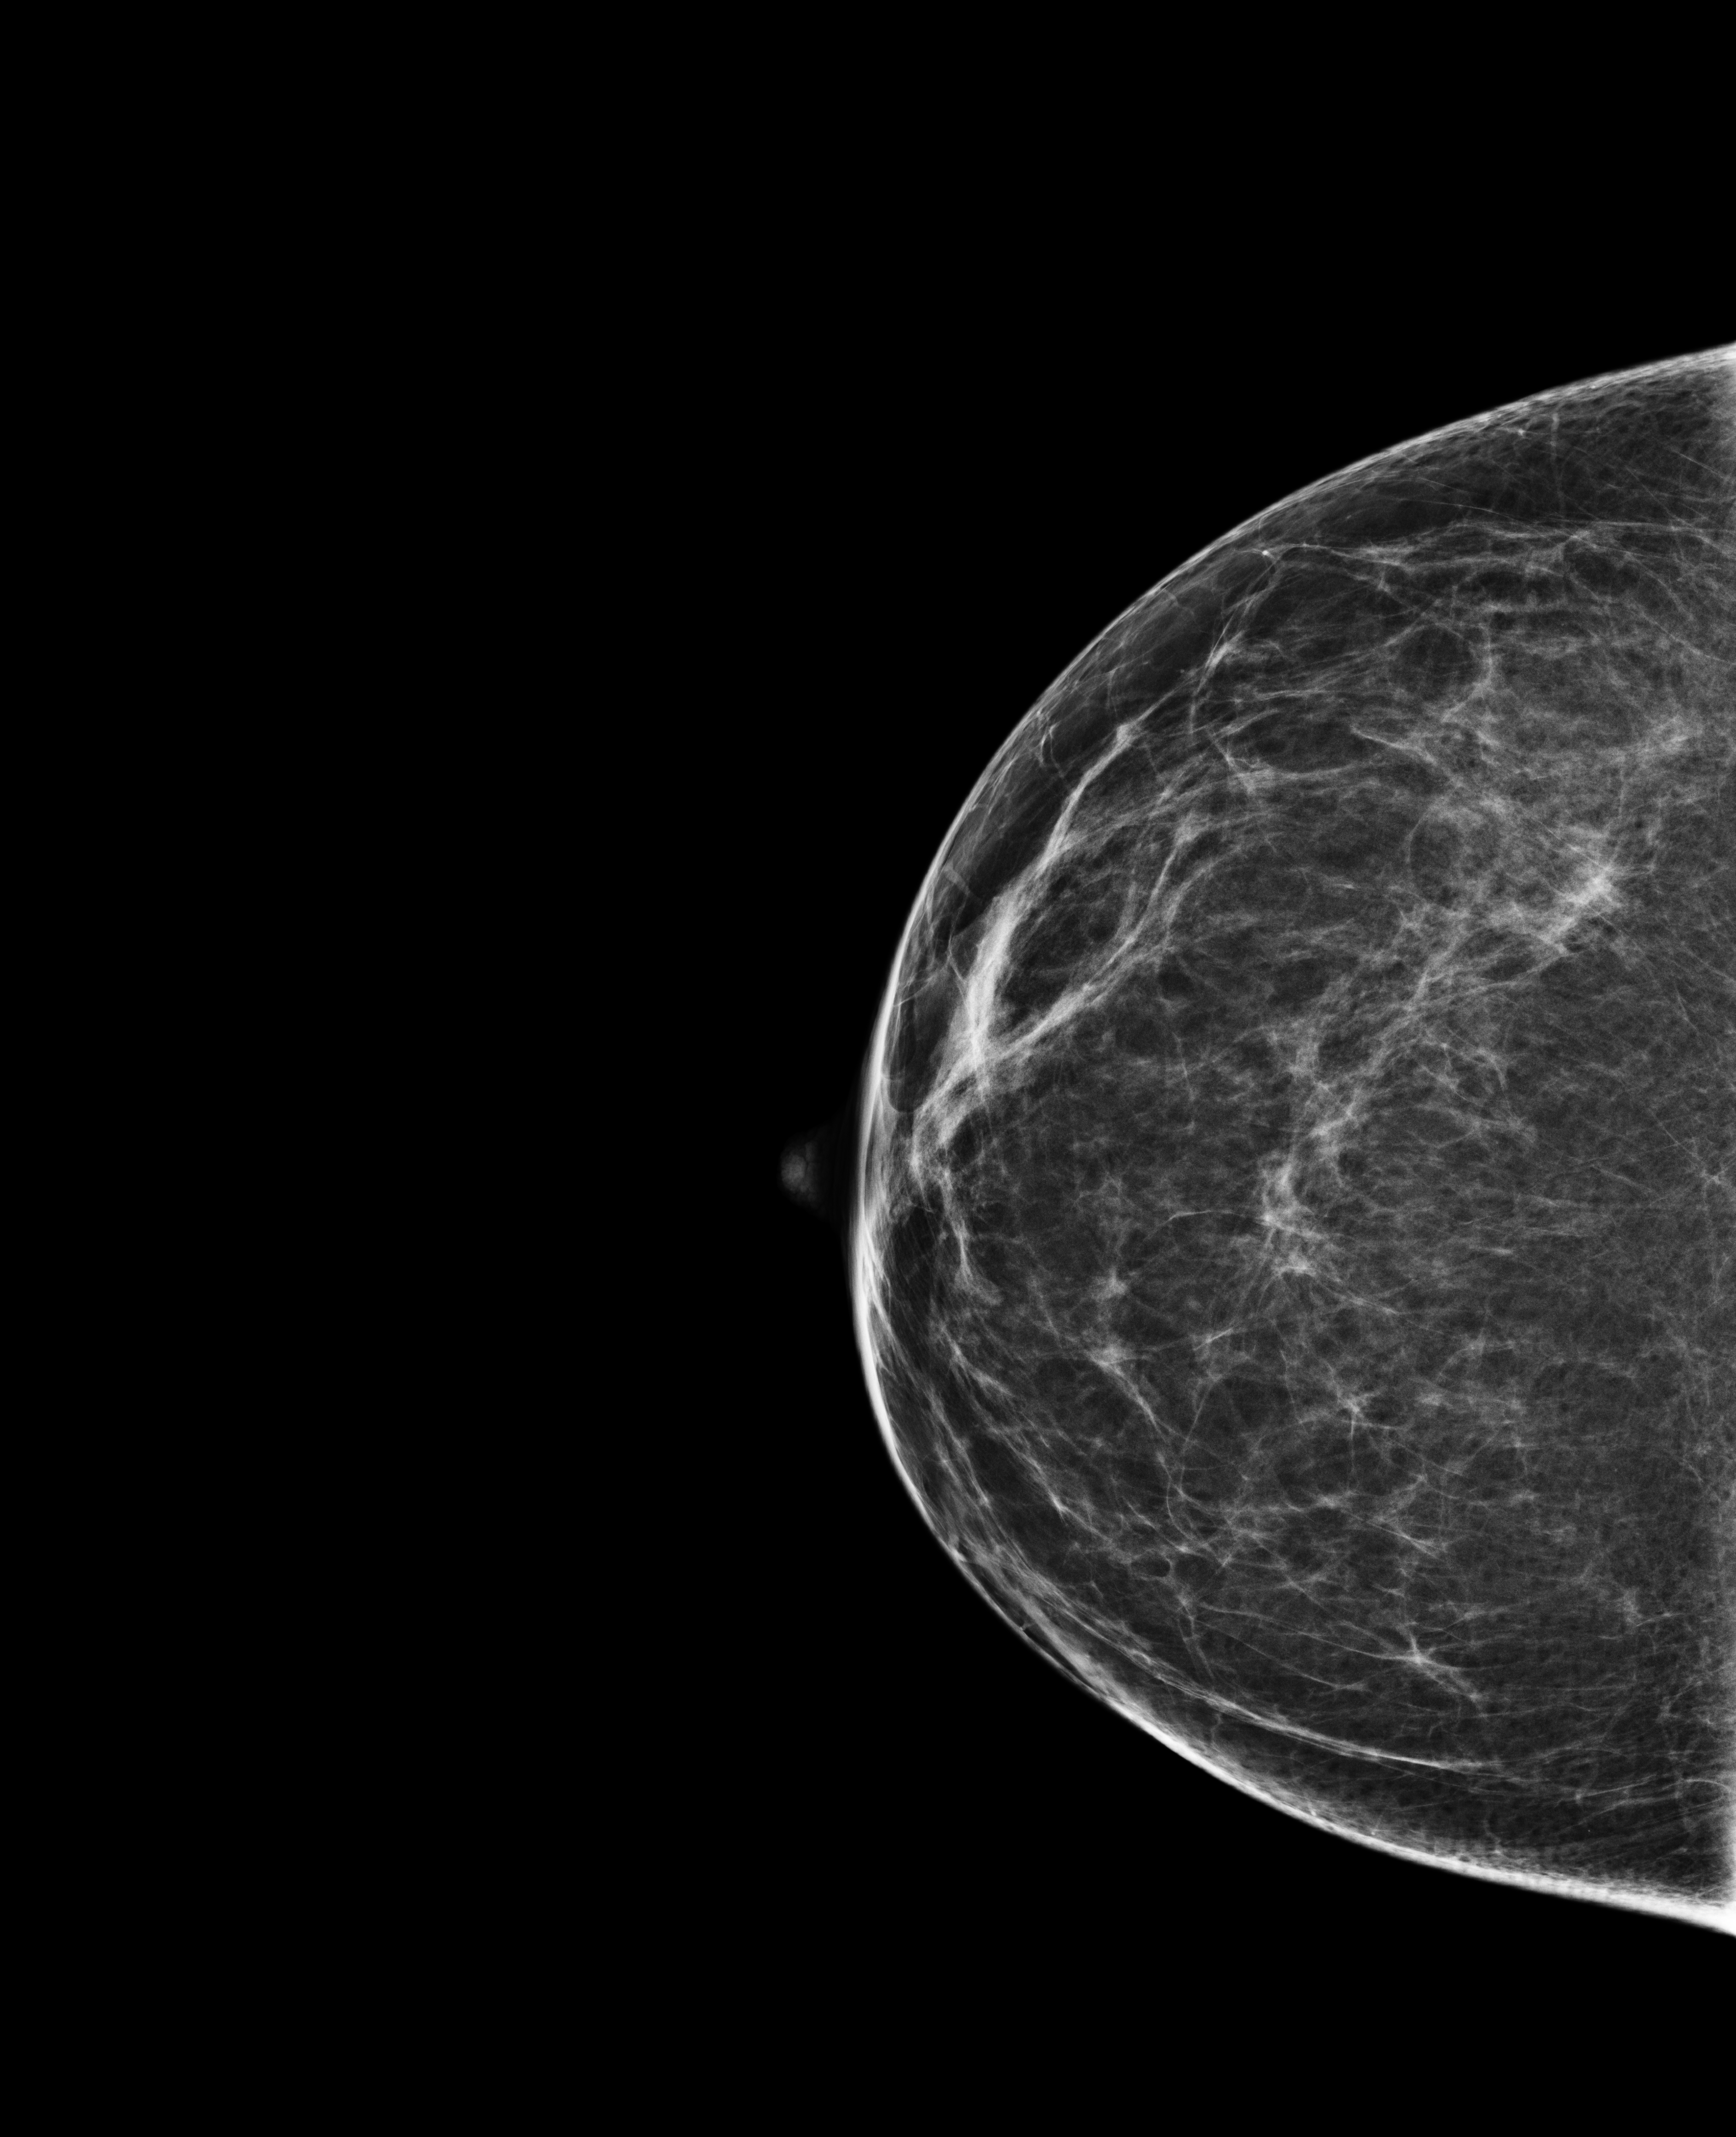
Annual screening mammography examination; system: Selenia Dimensions. Female patient, age 42 years.
Image type: full-field digital mammogram. Breast: right. Projection: cranio-caudal projection.